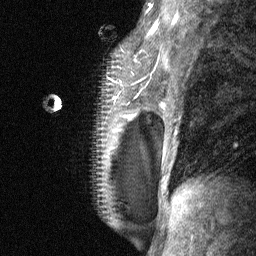
Breast MRI (dynamic contrast-enhanced), one sagittal slice. Position 47 of 64 along the scan axis. Dynamic contrast-enhanced study with each time point stored as its own series, time point 2 of 3 at this slice position (early post-contrast, ordered by acquisition time). 1.5 T. TE 4.8 ms, TR 27 ms. 256 × 256 image matrix. Patient: female, 34 years. From the clinical record (not read from this slice): setting: breast cancer imaged before/during neoadjuvant chemotherapy; receptor status: HR-positive, HER2-negative.
Outlined on this slice (semi-automatically segmented with operator editing):
- analysis volume of interest (the breast-tissue region the enhancement analysis was run in; not a lesion): bounding box [x1, y1, x2, y2] px = [43, 23, 157, 197]
- tumour enhancement mask (voxels above the 90 % enhancement threshold inside the analysis volume of interest): [114, 25, 155, 119]